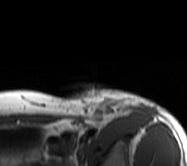
MRI of an extremity soft-tissue mass, one axial slice; position 48 of 62 along the scan axis; MR volume resampled by the dataset authors to the PET/CT grid (not the native acquisition matrix); 3.27 mm slice thickness; 187 × 166 image matrix, field of view 183 × 162 mm. Female patient. Case-level facts recorded for this patient, not image findings: histological type: leiomyosarcoma; grade: high; site of the primary tumour: groin.
Annotated regions visible in this slice (expert contour drawn on MRI and transferred to this co-registered scan by the dataset authors):
- gross tumour volume including surrounding oedema: box from (x=59, y=87) to (x=163, y=120) px
- gross tumour volume (mass): (x=87, y=101)–(x=113, y=120)